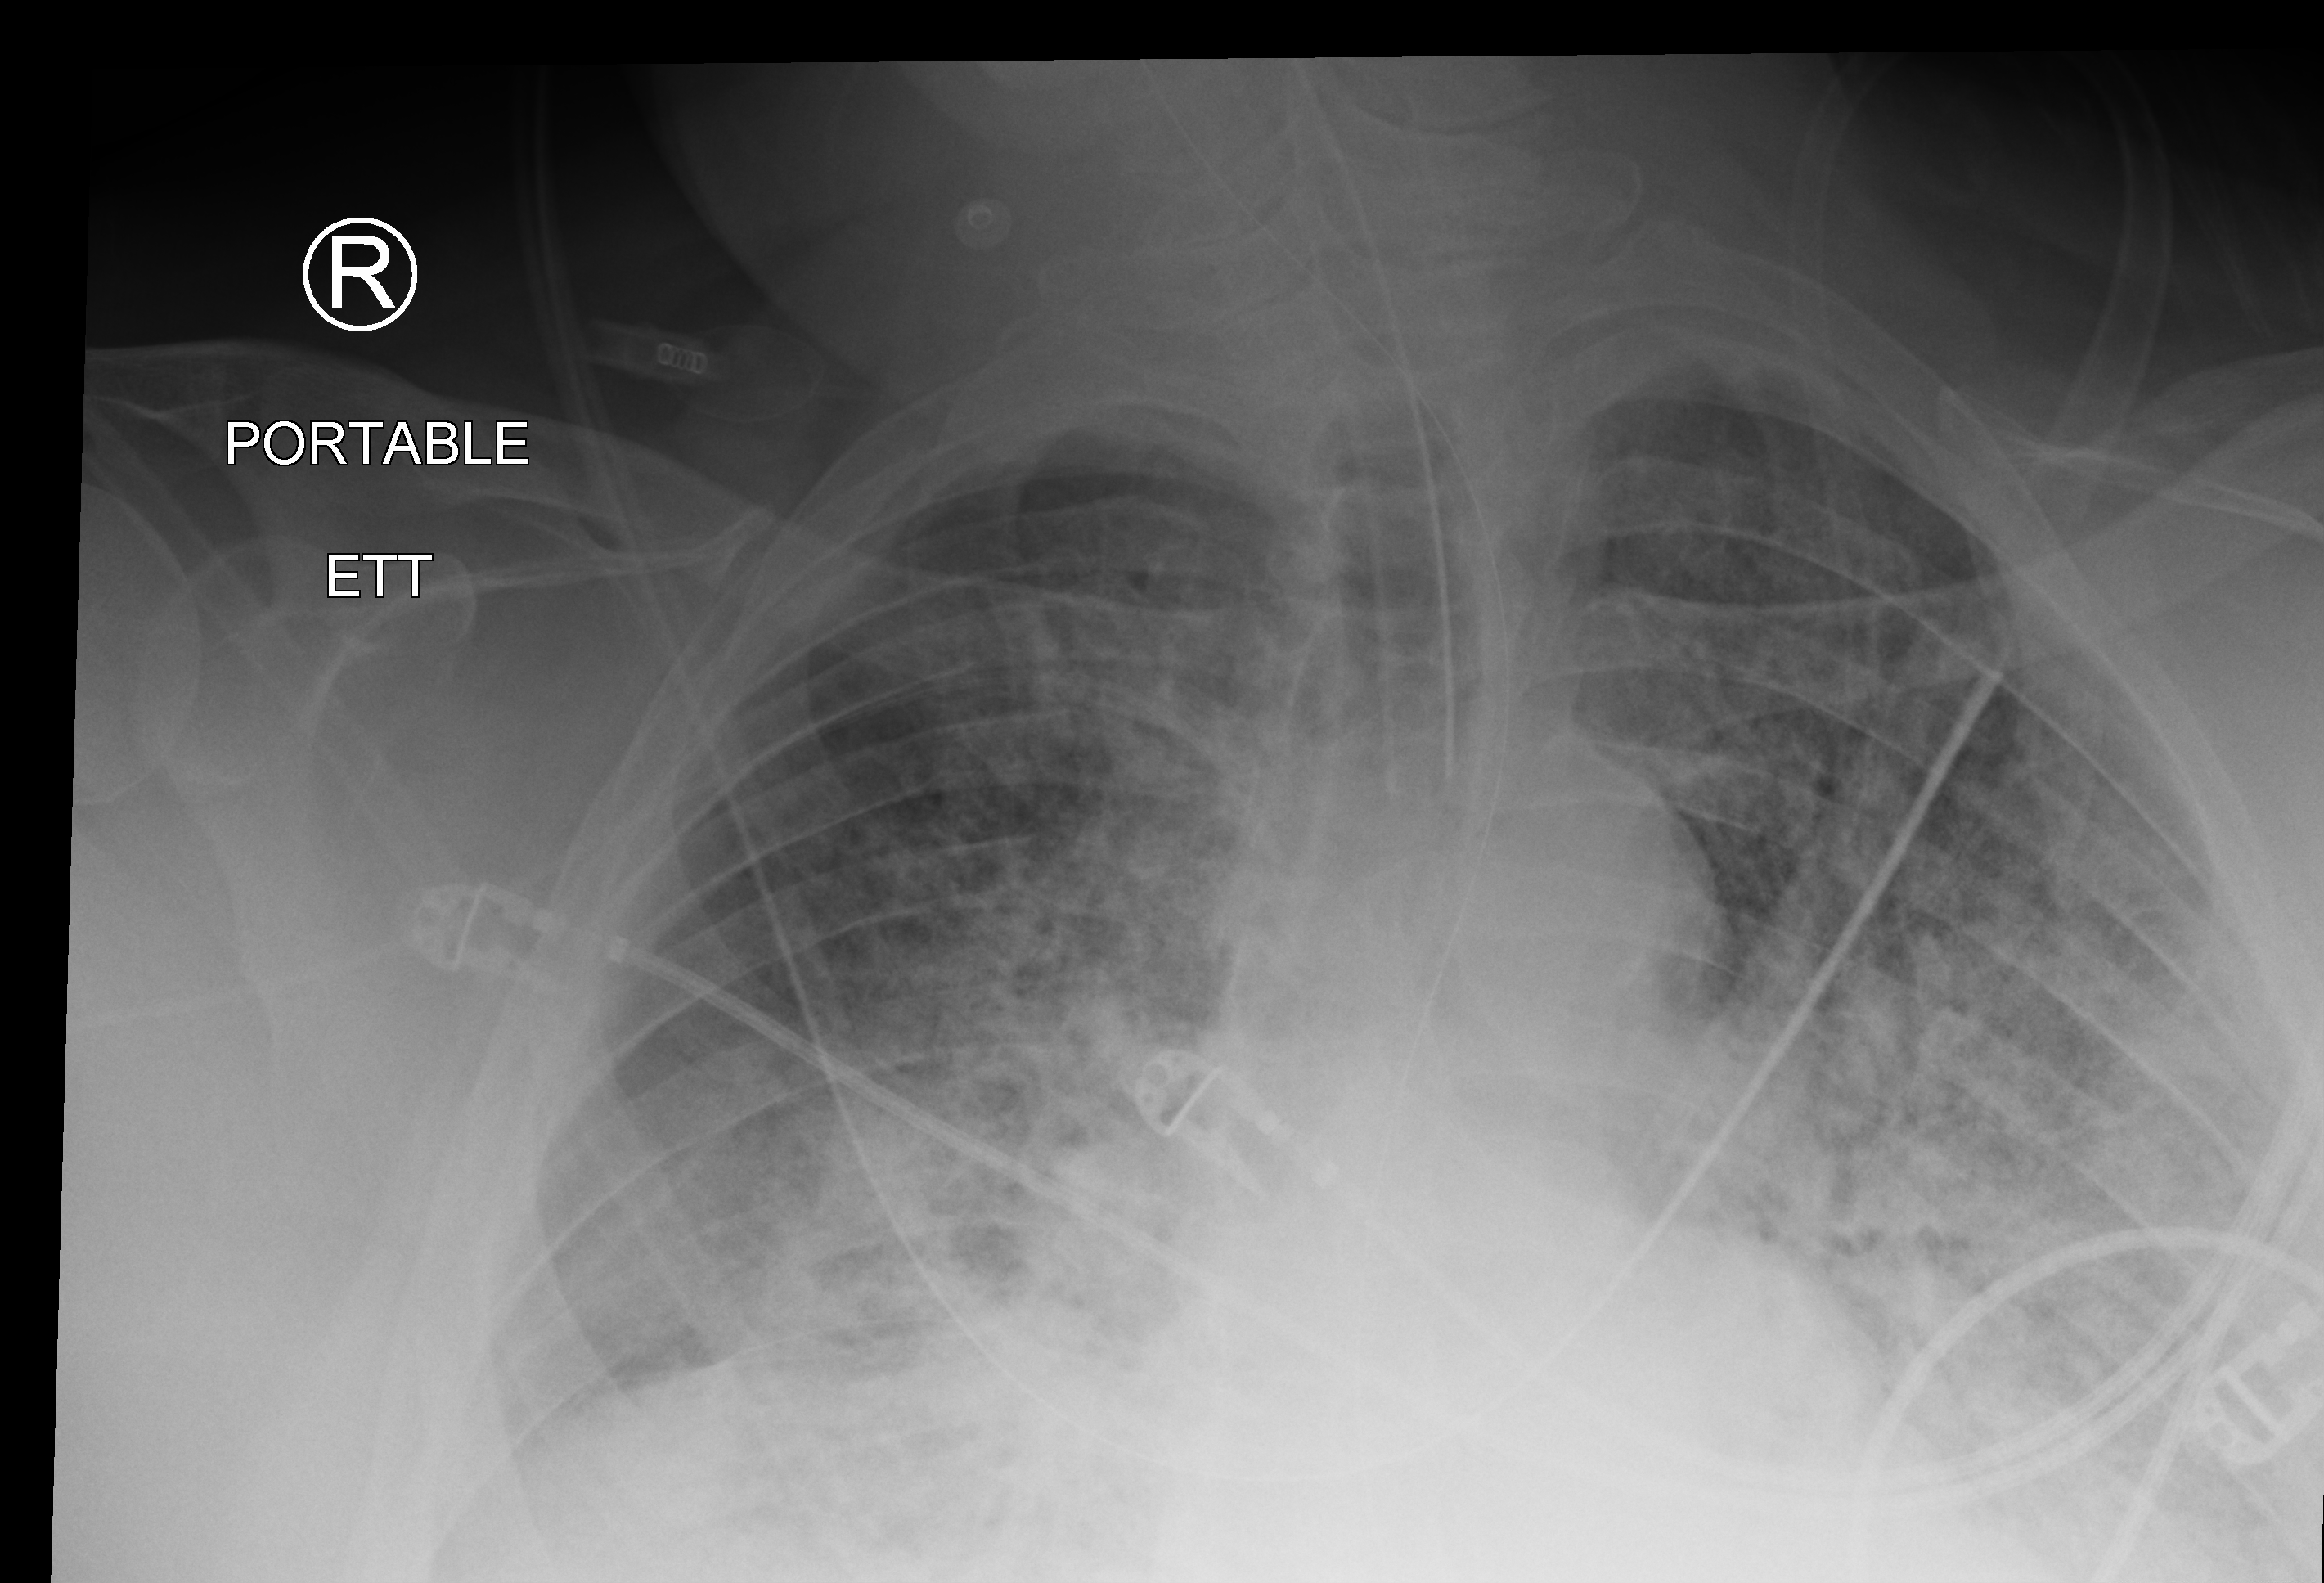
Bedside chest radiograph (computed radiography); anteroposterior (AP) projection. Male patient hospitalised with COVID-19, age 60–74 years.
Admission-level facts for this patient (not findings on this image; timing relative to this image not recorded):
- length of hospital stay: 13 days
- chronic kidney disease (admission record): no
- mechanically ventilated during this hospital stay: yes